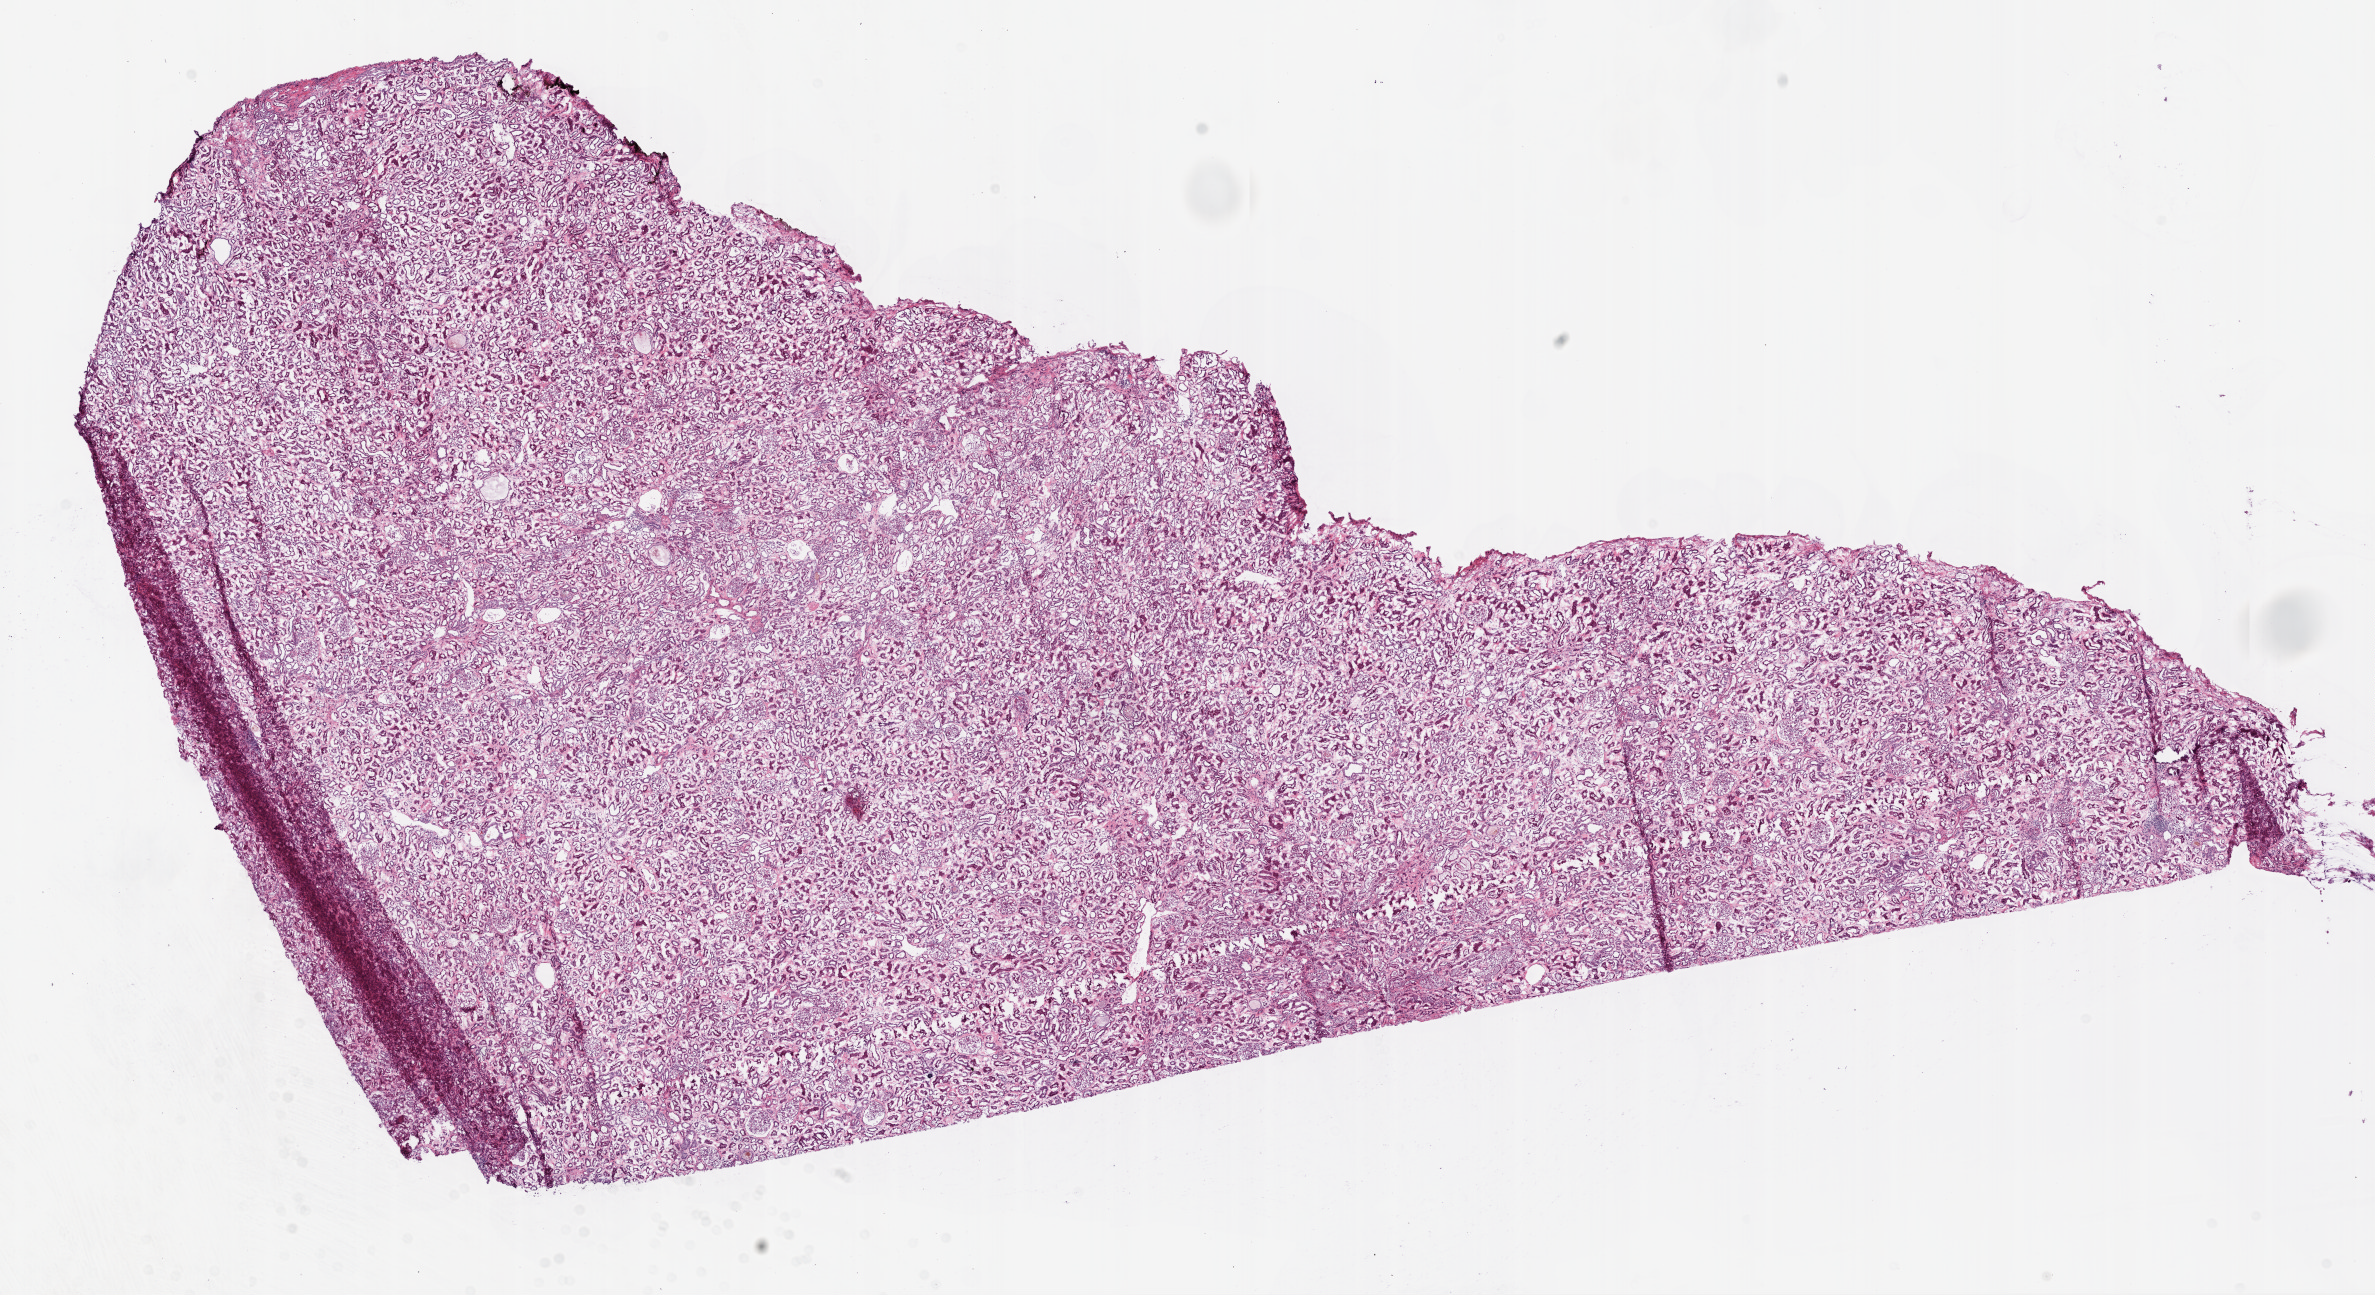
Digitized H&E tissue section (whole slide) — whole scanned area (about 19.1 x 10.4 mm) shown as a low-resolution overview, frozen section from the top of the tissue portion, kidney, solid tissue normal (non-tumour tissue) sample. Patient: male, age at initial diagnosis 64 years.
This section: solid tissue normal sample (biorepository sample class). Patient diagnosis: Clear cell adenocarcinoma, NOS.